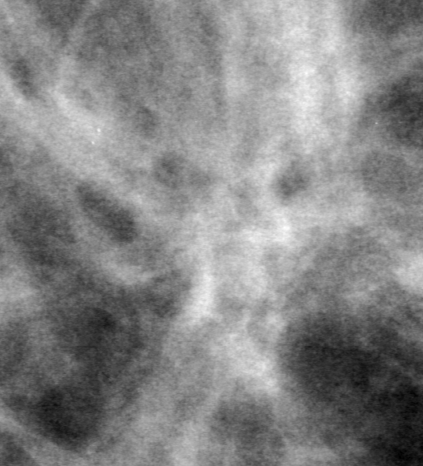
Cropped region of a digitized screen-film mammogram centred on a radiologist-marked abnormality; left breast; CC view.
Finding: mass, shape architectural distortion, margins ill defined; BI-RADS assessment category 4; pathology (as recorded): benign.